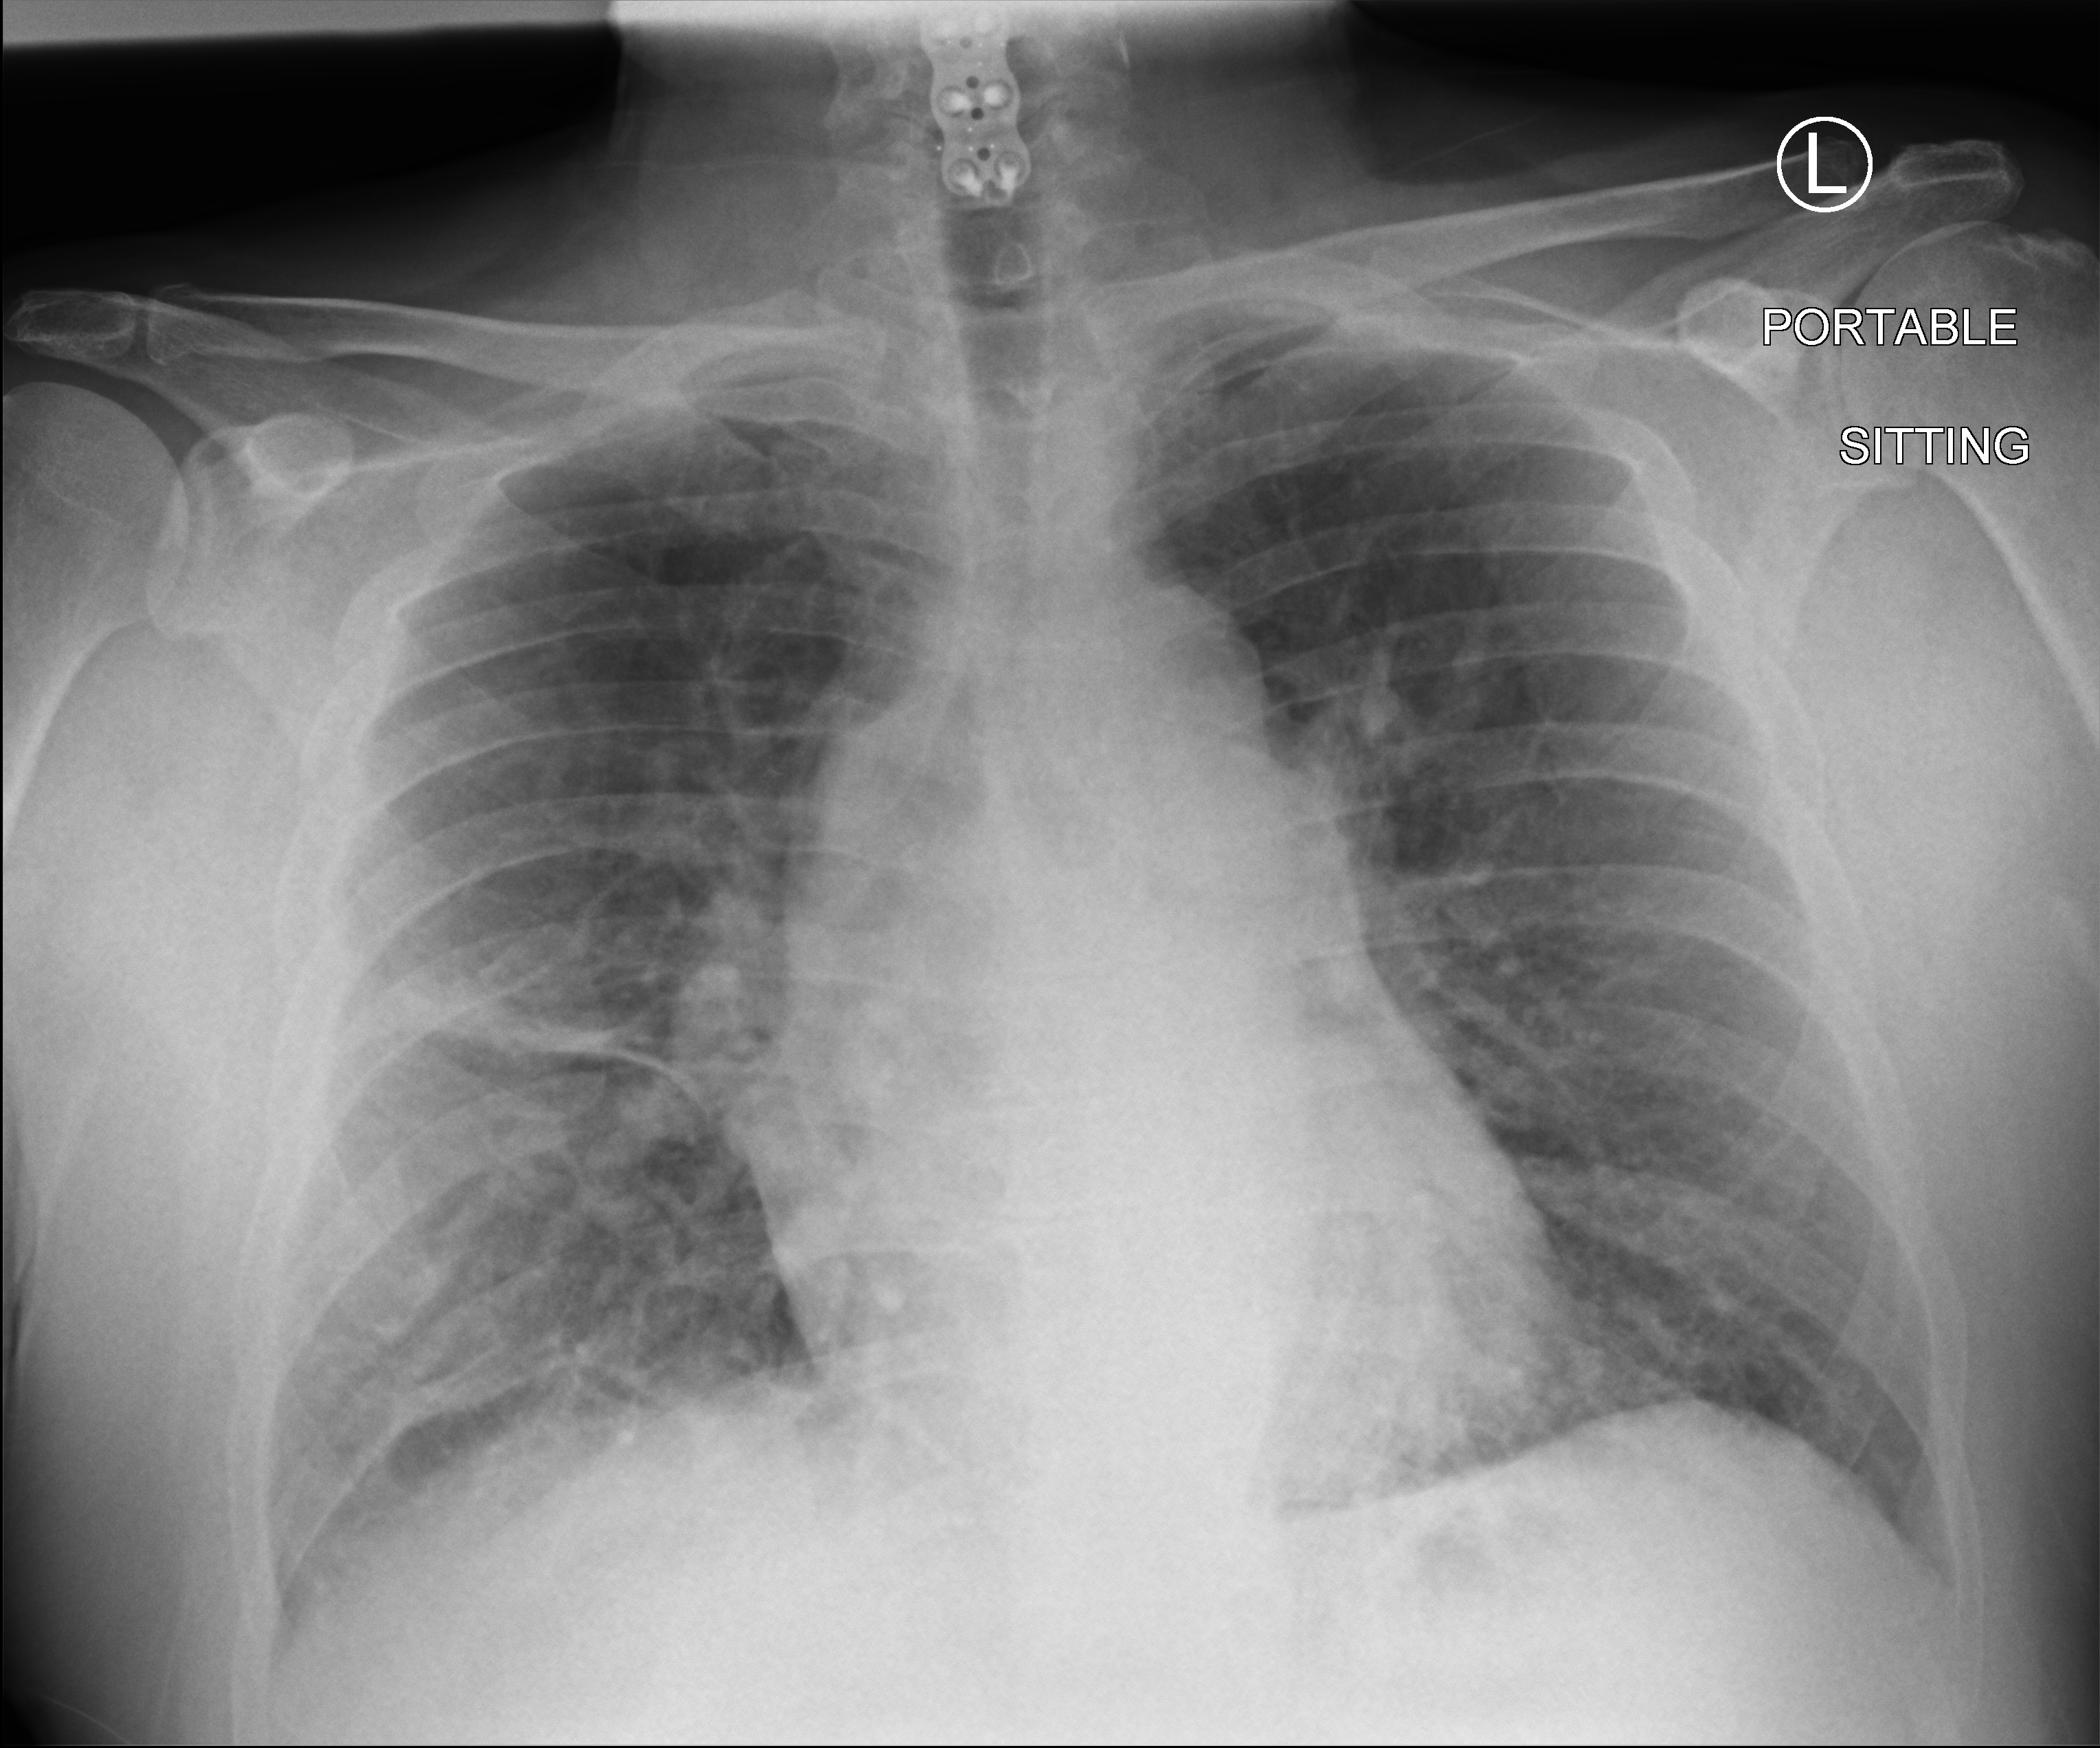
Bedside chest radiograph (computed radiography). Male patient hospitalised with COVID-19, age 18–59 years.
Hospital-stay facts (about this admission, not read from this image; timing relative to this image not recorded): mechanically ventilated during this hospital stay: no.